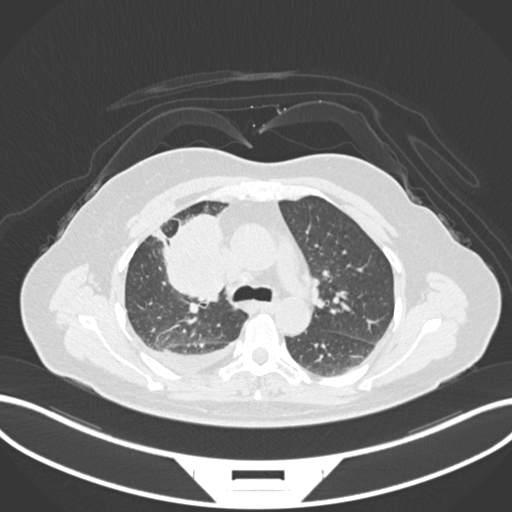
Chest CT, one axial slice. Position 100 of 172 along the scan axis. Reconstruction kernel B30f. 120 kVp. Lung window (W 1500 / L -600 HU). 1 mm slice thickness. 512 × 512 image matrix, field of view 400 × 400 mm. Patient: female, 52 years. Case-level facts recorded for this patient, not image findings: clinical TNM (as recorded): T3 N1 M1.
Annotated regions visible in this slice (bounding box drawn by a radiologist):
- lung tumour (recorded histology: adenocarcinoma): bounding box <154,213,232,305> (left, top, right, bottom; pixels)